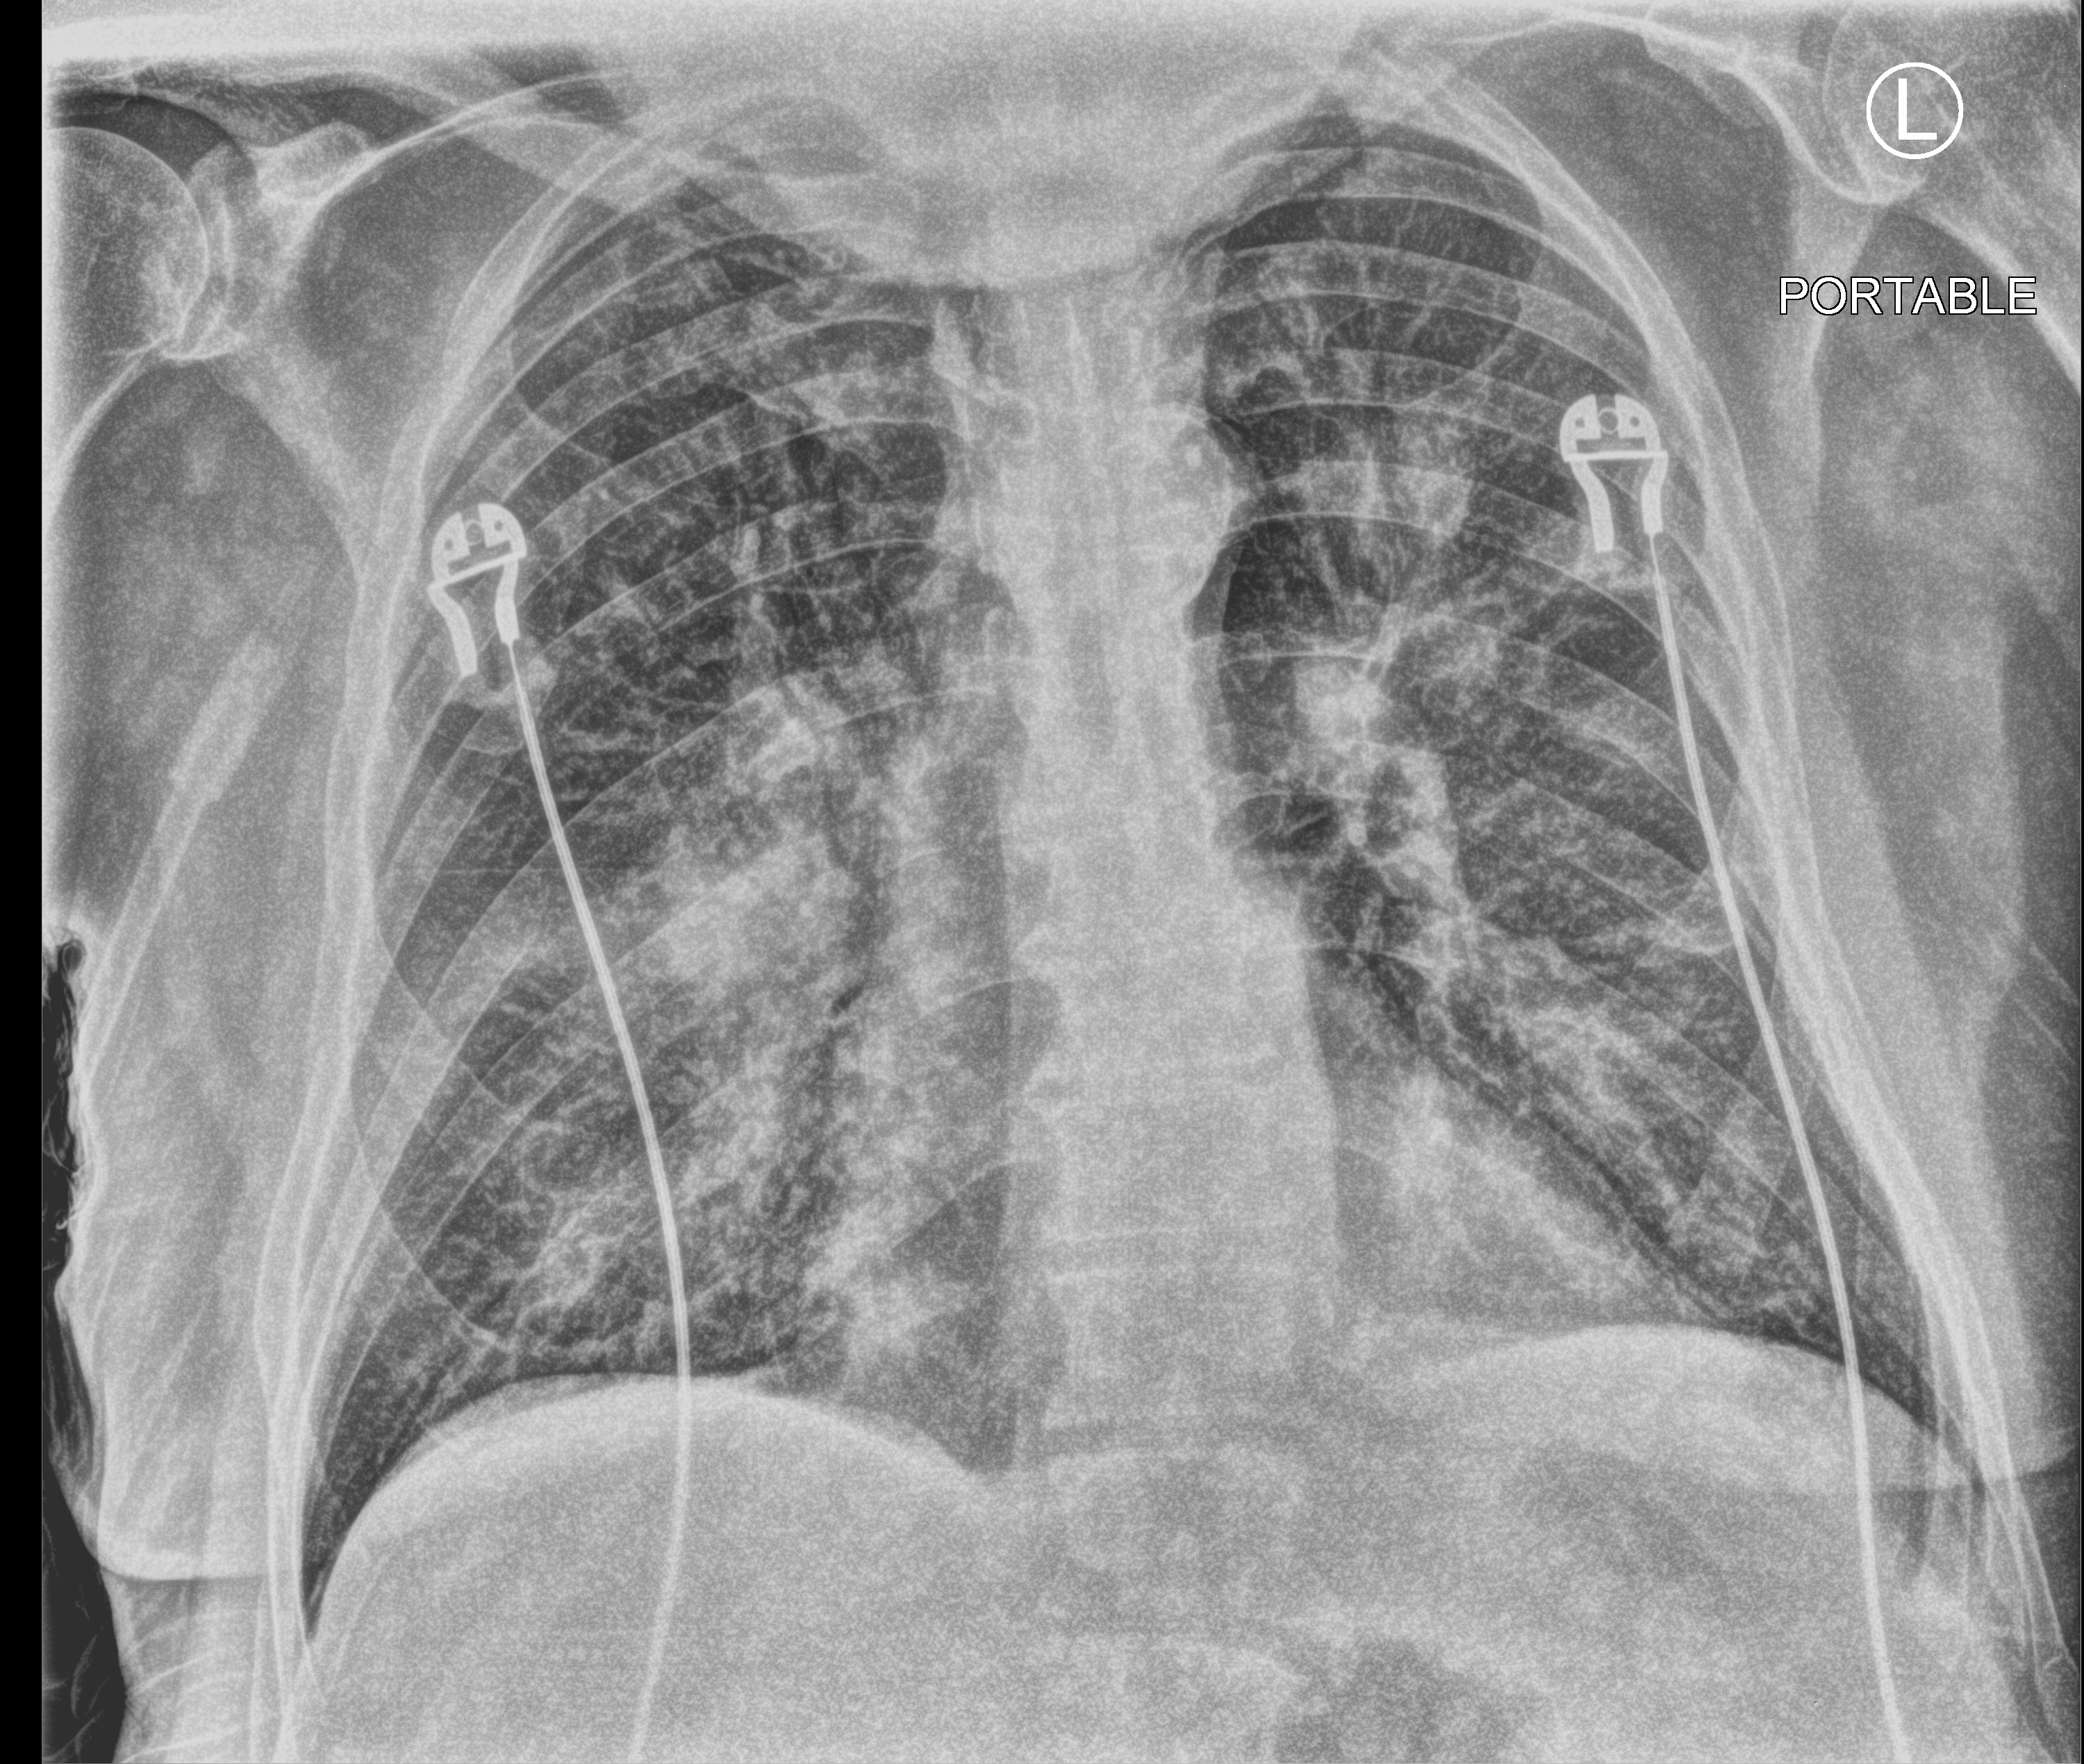
Chest X-ray (portable), anteroposterior (AP) projection. Male patient hospitalised with COVID-19, age 60–74 years.
Admission-level facts for this patient (not findings on this image; timing relative to this image not recorded): chronic kidney disease (admission record): yes; mechanically ventilated during this hospital stay: yes.